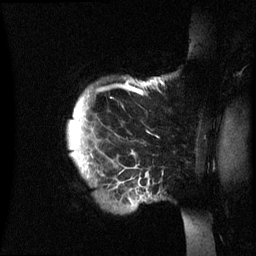
Breast MRI (dynamic contrast-enhanced), one sagittal slice; position 55 of 60 along the scan axis; dynamic contrast-enhanced series, image 2 of 3 at this slice position (ordered by acquisition); 1.5 T; TE 4.2 ms, TR 8.4 ms; 2.4 mm slice thickness; 256 × 256 image matrix. Female patient, age 48 years.
Outlined on this slice (semi-automatic segmentation, software-assisted and operator-edited):
- analysis volume of interest (the breast-tissue region the enhancement analysis was run in; not a lesion): box from (x=68, y=78) to (x=195, y=235) px
- tumour enhancement mask (voxels above the 70 % enhancement threshold inside the analysis volume of interest): (x=73, y=82)–(x=149, y=169)